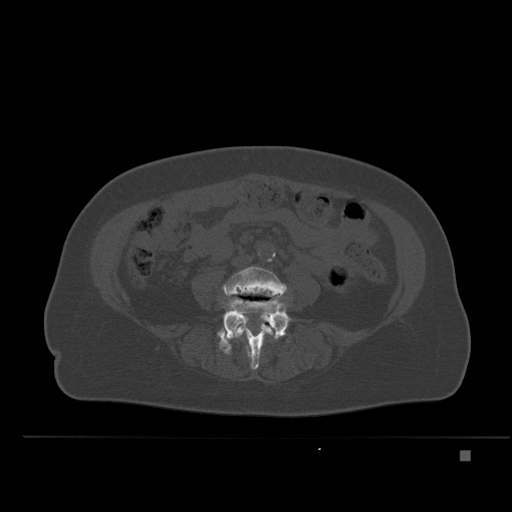
CT including the spine, one axial slice; slice 169 of 477 in the series (ordered by position); bone window (W 1800 / L 400 HU); 512 × 512 image matrix, field of view 422 × 422 mm. Female patient, age 74 years. From the clinical record (not read from this slice): primary cancer: colon.
Structures marked on this image (semi-automatic segmentation, software-assisted and operator-edited):
- L4 vertebra: bounding box [x1, y1, x2, y2] px = [222, 266, 288, 338]
- L5 vertebra: [218, 298, 290, 369]